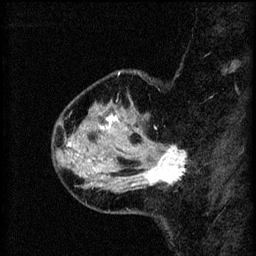
Breast MRI (dynamic contrast-enhanced), one sagittal slice. Position 16 of 60 along the scan axis. 3 images stored at this slice position (order not interpretable as contrast timing). 1.5 T. TE 4.2 ms, TR 8.2 ms. 256 × 256 image matrix, field of view 180 × 180 mm. Female patient, age 37 years.
Structures marked on this image (semi-automatically segmented with operator editing):
- analysis volume of interest (the breast-tissue region the enhancement analysis was run in; not a lesion): bounding box [x1, y1, x2, y2] px = [124, 138, 187, 191]
- tumour enhancement mask (voxels above the 70 % enhancement threshold inside the analysis volume of interest): [128, 146, 186, 187]